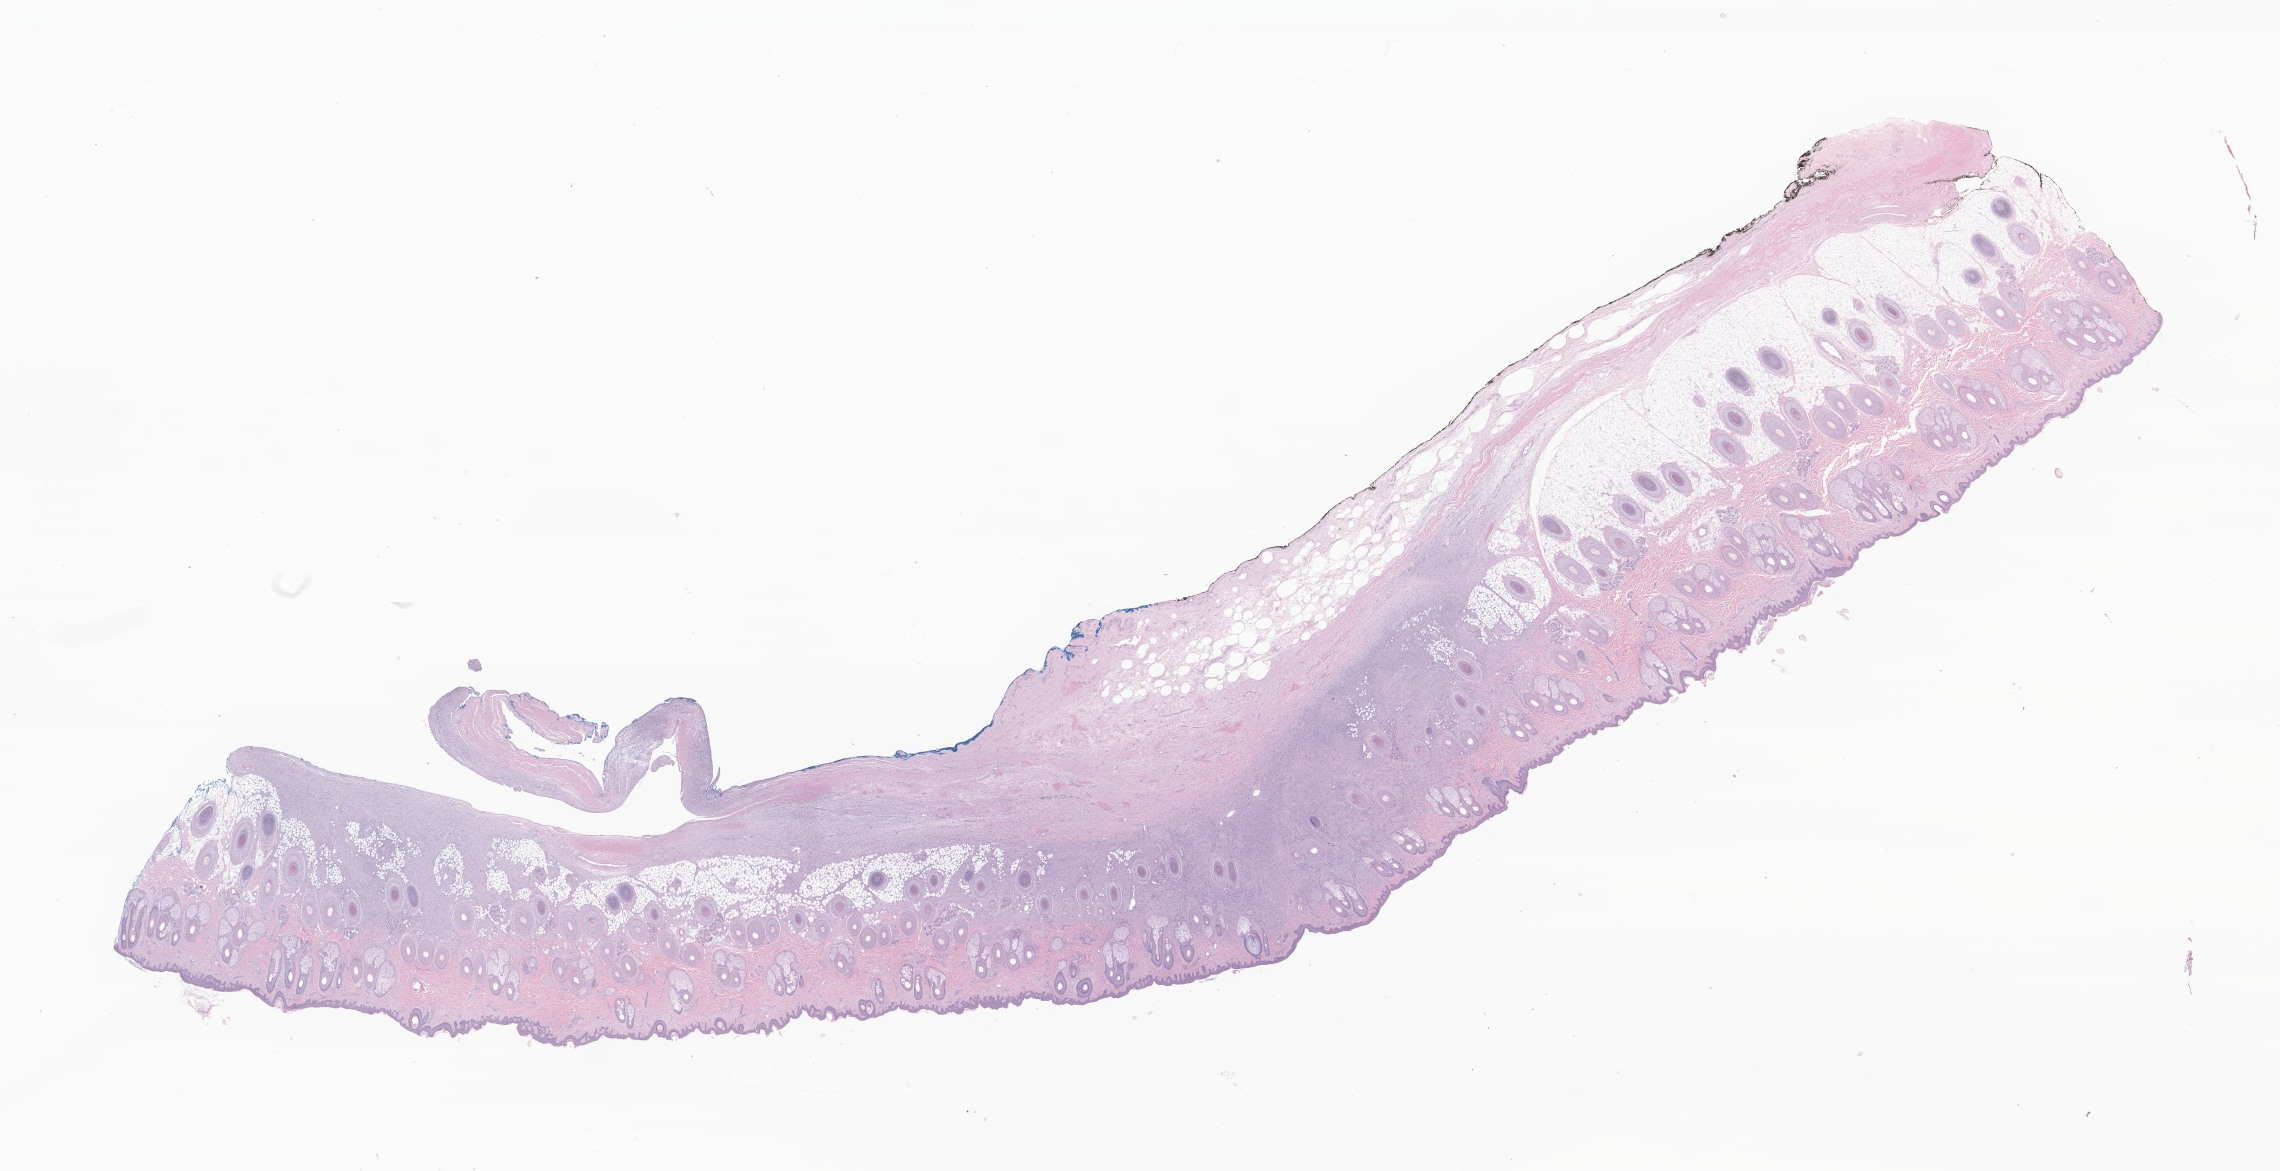
Digitized hematoxylin and eosin (H&E)-stained section of tumor tissue from the skin of scalp and neck — low-resolution overview of the scanned area, about 38.5 x 19.7 mm, formalin-fixed paraffin-embedded section. Patient female; age 196 months (16 years 4 months).
* diagnosis: Dermatofibrosarcoma protuberans, fibrosarcomatous